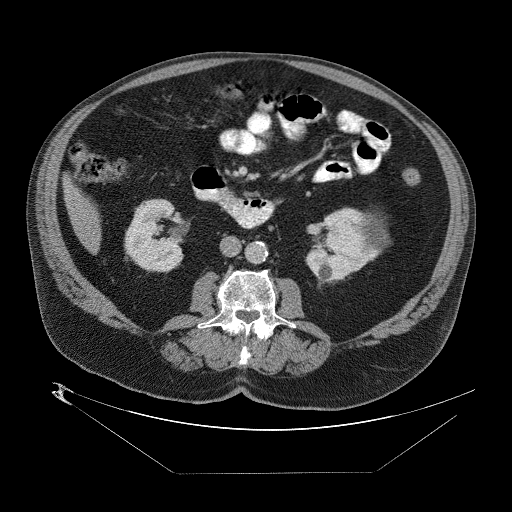
Contrast-enhanced abdominal CT (liver protocol), one axial slice. Slice 8 of 89 in the series (ordered by position). 140 kVp. One of 2 acquisitions stored at this slice position. Soft-tissue window (W 400 / L 40 HU). 2.5 mm slice thickness. 512 × 512 image matrix, field of view 480 × 480 mm. Case-level facts recorded for this patient, not image findings: diagnosis: hepatocellular carcinoma (patient treated with transarterial chemoembolisation; whether this scan precedes or follows treatment is not stated here); TNM stage (as recorded): Stage-II.
Annotated regions visible in this slice (semi-automatically segmented with operator editing):
- abdominal aorta: bounding box <246,242,268,265> (left, top, right, bottom; pixels)
- liver parenchyma outside the tumour (the mass and vessels are separate outlines, so this box may not span the whole liver): <62,171,100,244>